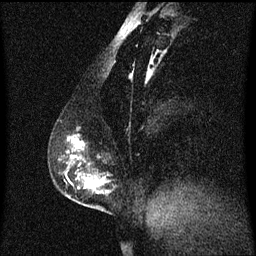
Breast MRI (dynamic contrast-enhanced), one sagittal slice; slice 26 of 60 in the series (ordered by position); dynamic contrast-enhanced series, image 2 of 3 at this slice position (ordered by acquisition); 1.5 T; TE 4.2 ms, TR 8.4 ms; 2 mm slice thickness; 256 × 256 image matrix. Female patient, age 40 years. Case-level facts recorded for this patient, not image findings: setting: breast cancer imaged before/during neoadjuvant chemotherapy; receptor status: triple-negative.
Outlined on this slice (semi-automatically segmented with operator editing):
- analysis volume of interest (the breast-tissue region the enhancement analysis was run in; not a lesion): bounding box (x1, y1, x2, y2) in pixels: (58, 136, 111, 211)
- tumour enhancement mask (voxels above the 70 % enhancement threshold inside the analysis volume of interest): (72, 138, 107, 193)